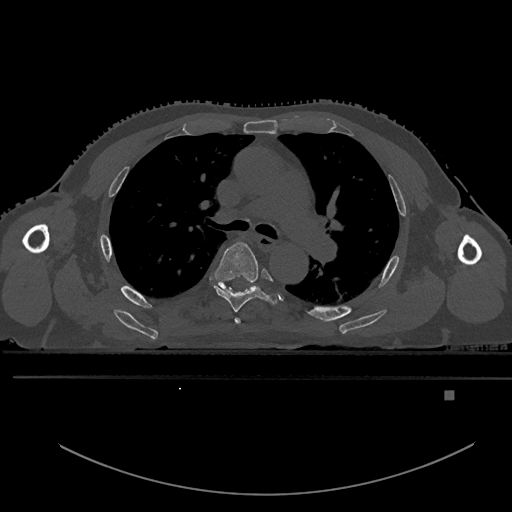
CT including the spine, one axial slice. Slice 355 of 969 in the series (ordered by position). Bone window (W 1800 / L 400 HU). 0.5 mm slice thickness. 512 × 512 image matrix. Patient: male, 82 years. Case-level facts recorded for this patient, not image findings: primary cancer: prostate; vertebrae with lytic lesions (as recorded): T11, T9, T8, T2.
Annotated regions visible in this slice (semi-automatic segmentation, software-assisted and operator-edited):
- T4 vertebra: bounding box [x1, y1, x2, y2] px = [234, 317, 241, 324]
- T5 vertebra: [214, 241, 278, 312]
- T6 vertebra: [214, 283, 250, 292]